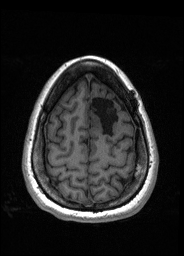
Pre-operative brain MRI before brain-tumour surgery, one axial slice. Slice 45 of 176 in the series (ordered by position). T1-weighted post-contrast. 1 mm slice thickness. 184 × 256 image matrix, field of view 180 × 250 mm. From the clinical record (not read from this slice): histopathology: Oligodendroglioma; WHO grade: 2; IDH mutation: yes; tumour location: Left Frontal.
Structures marked on this image (expert manual segmentation):
- tumour: bounding box <90,108,113,126> (left, top, right, bottom; pixels)